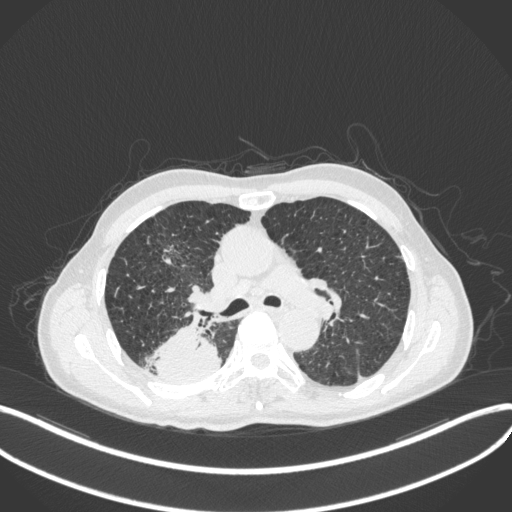
Chest CT, one axial slice; position 290 of 423 along the scan axis; reconstruction kernel B31f; 120 kVp; lung window (W 1500 / L -600 HU); 1 mm slice thickness; 512 × 512 image matrix. Male patient, age 79 years. Case-level facts recorded for this patient, not image findings: clinical TNM (as recorded): T3 N0 M0.
Annotated regions visible in this slice (rectangle marked by the reading radiologist):
- lung tumour (recorded histology: adenocarcinoma): bounding box <146,317,223,385> (left, top, right, bottom; pixels)